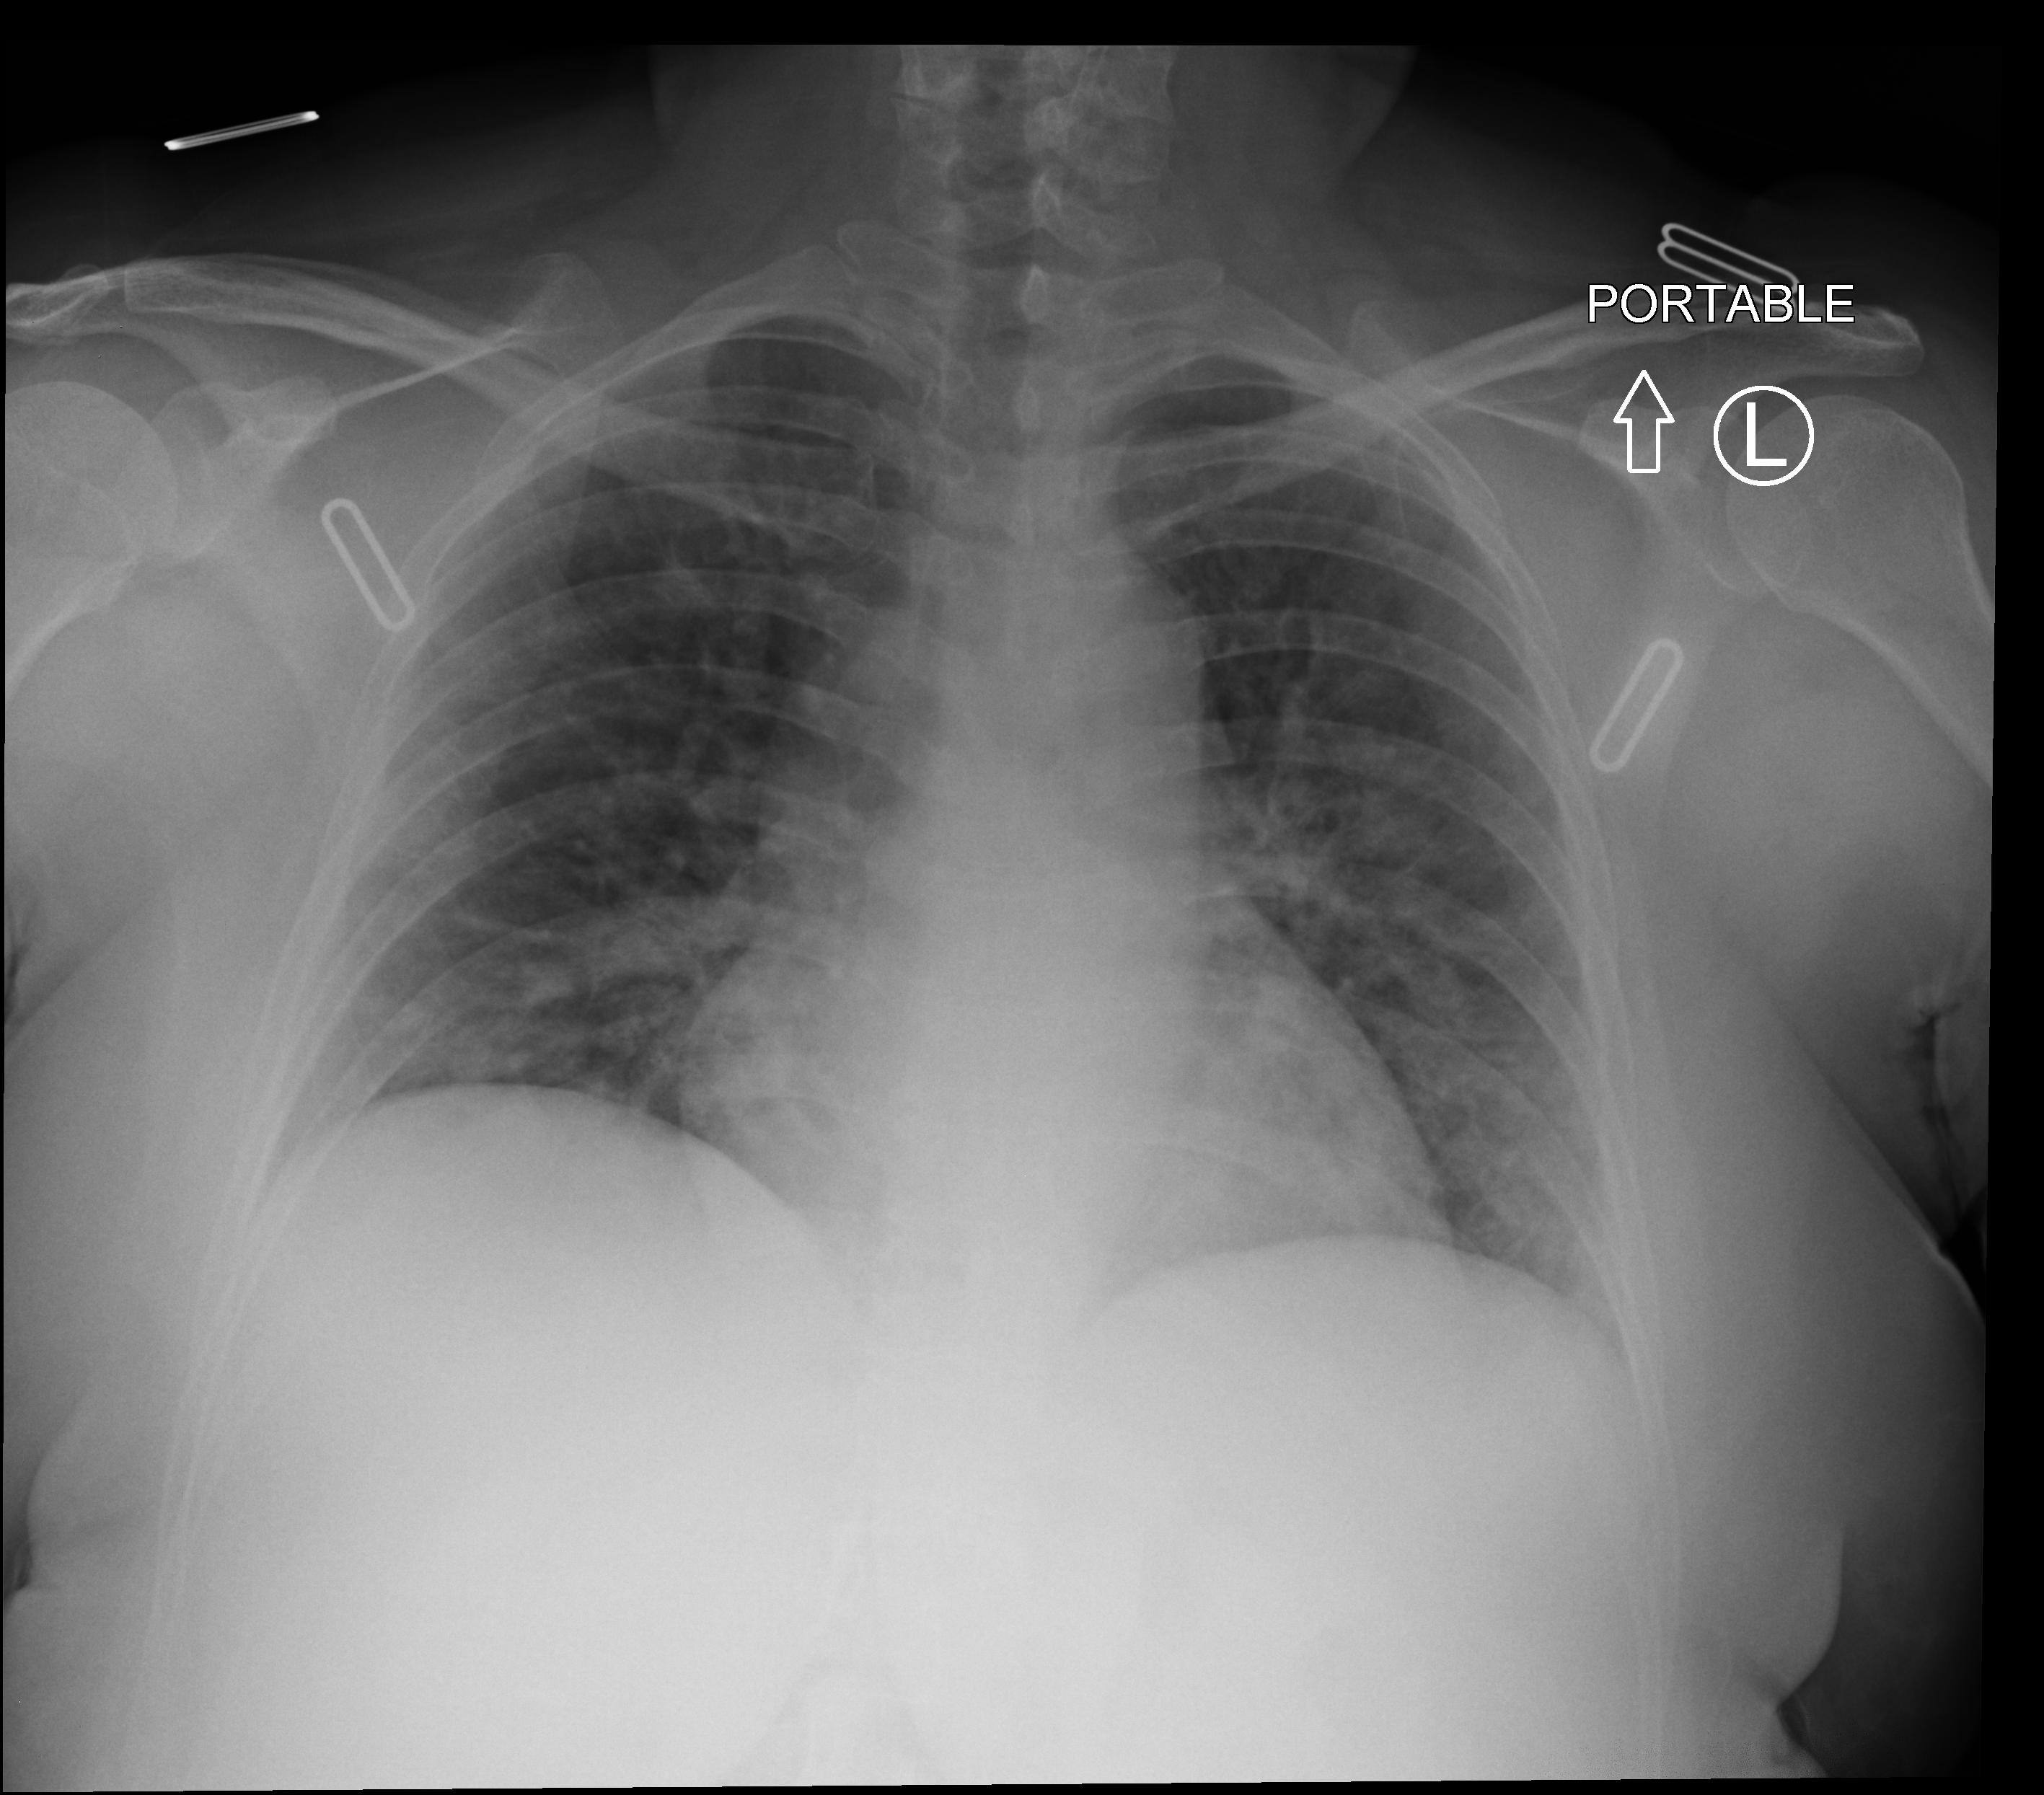
Portable chest radiograph. Patient hospitalised with COVID-19; female, aged 18–59 years.
Hospital-stay facts (about this admission, not read from this image; timing relative to this image not recorded):
- admitted to intensive care during this hospital stay: no
- mechanically ventilated during this hospital stay: no
- chronic kidney disease (admission record): no